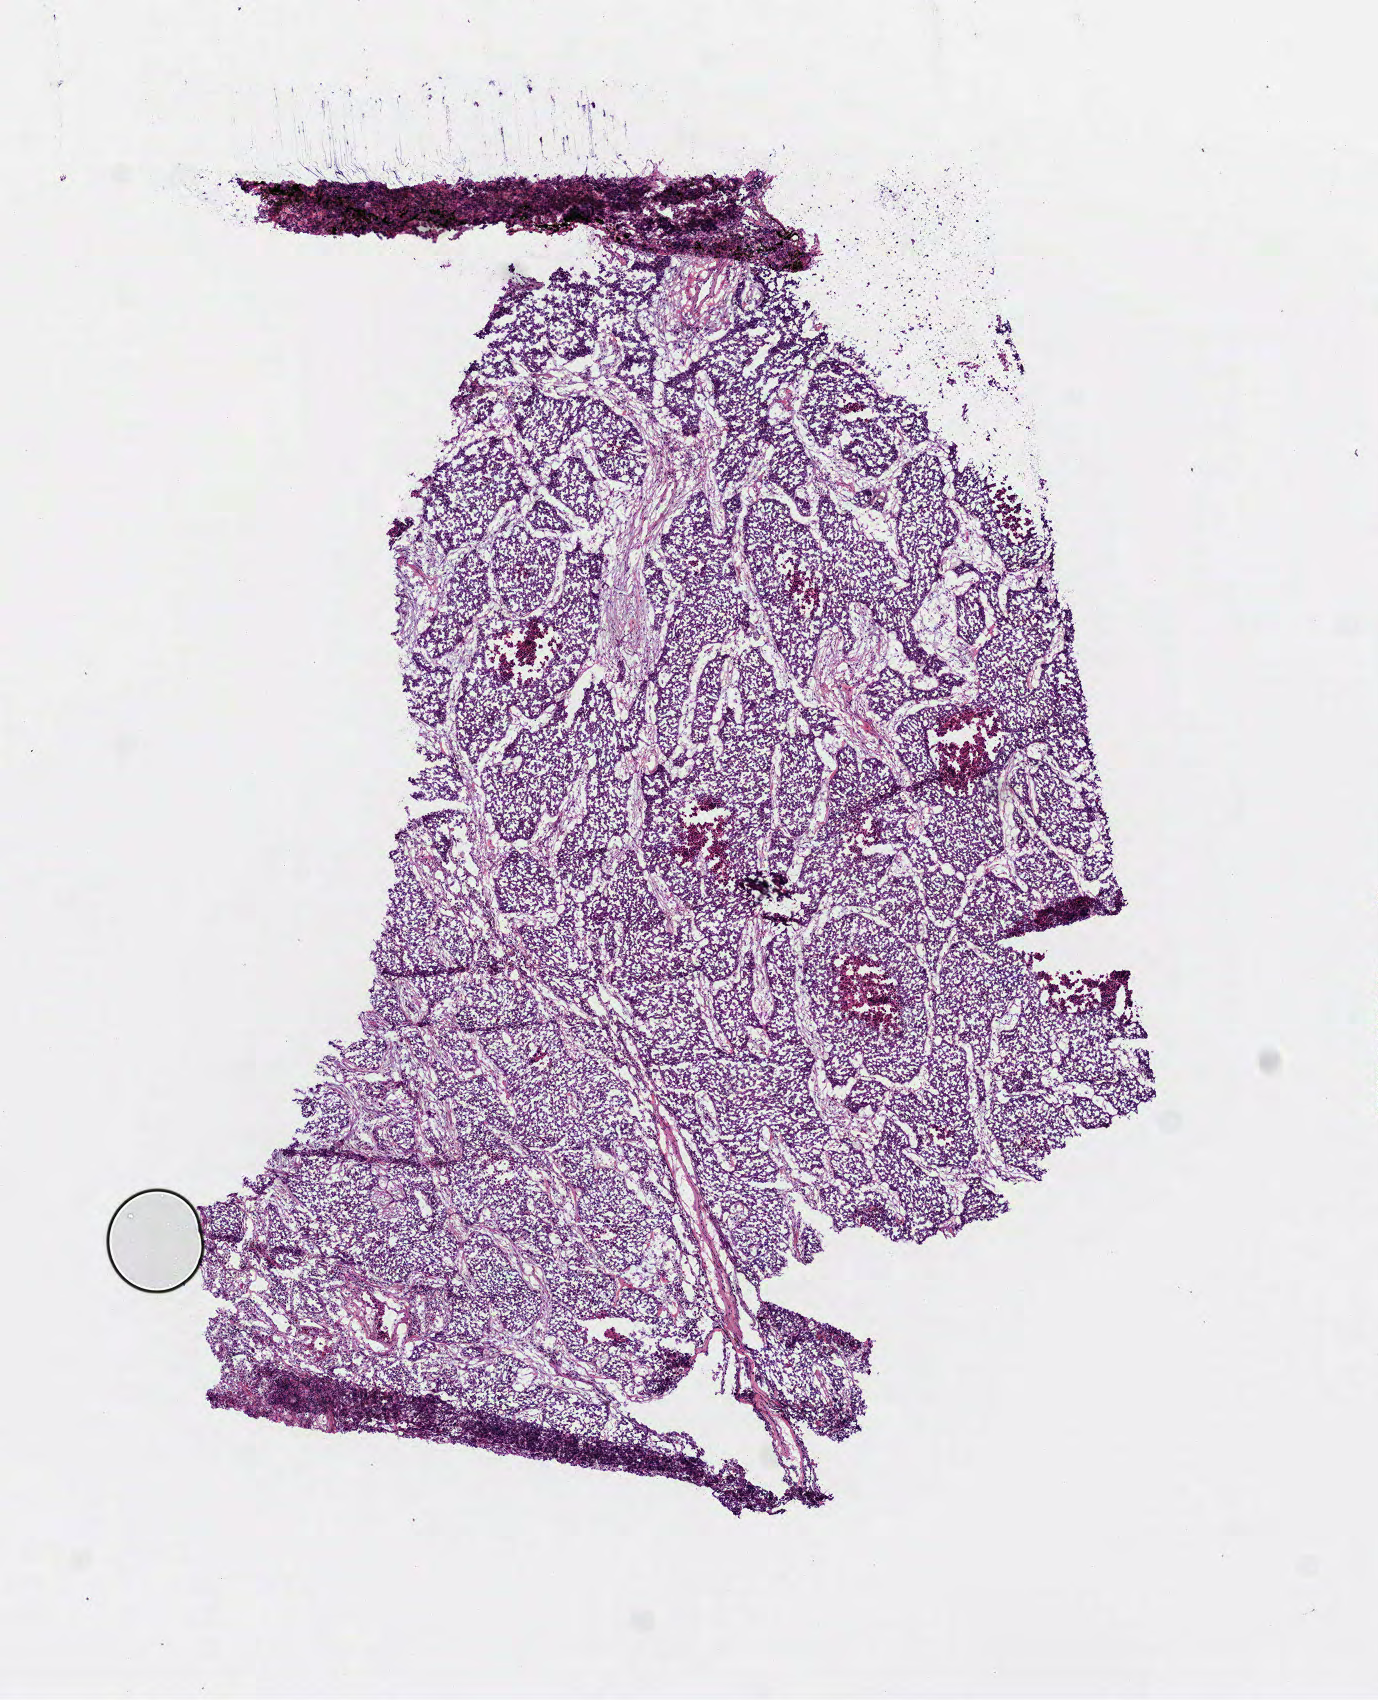
Digitized H&E tissue section (whole slide), a low-resolution overview of the entire scanned area, about 5.6 x 6.9 mm; frozen section; primary tumour sample from the lung. Male, age 74 years at initial diagnosis. Pathologist review of this section (percent, as recorded): tumour cells 95%, tumour nuclei 85%, normal cells 0%, stromal cells 0%, necrosis 5%. Infiltration values recorded for this section: lymphocyte infiltration 2%, monocyte infiltration 2%, neutrophil infiltration 2%.
AJCC pathologic stage: IB (6th edition). Laterality: right. Pathologic diagnosis: Basaloid squamous cell carcinoma (upper lobe, lung).